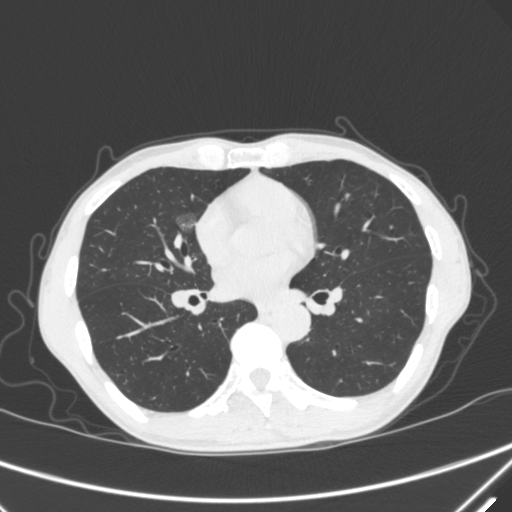
Chest CT, one axial slice. Position 163 of 340 along the scan axis. Lung window (W 1500 / L -600 HU). 512 × 512 image matrix. Male patient, age 67 years. From the clinical record (not read from this slice): clinical TNM (as recorded): T1c N0 M0.
Structures marked on this image (rectangle marked by the reading radiologist):
- lung tumour (recorded histology: adenocarcinoma): box from (x=168, y=208) to (x=200, y=239) px